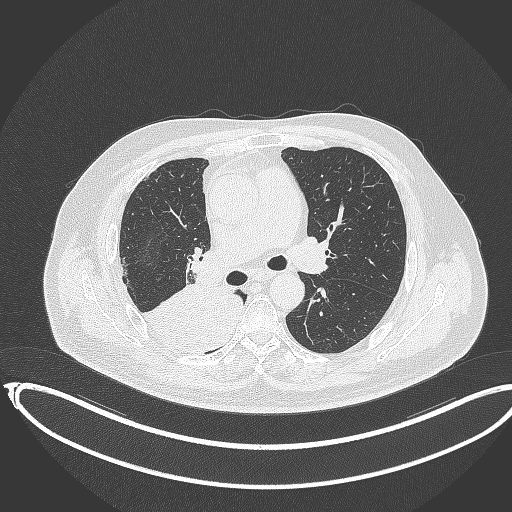
Chest CT, one axial slice. Position 211 of 403 along the scan axis. 120 kVp. Lung window (W 1500 / L -600 HU). 1 mm slice thickness. 512 × 512 image matrix, field of view 436 × 436 mm. Male patient, age 68 years. From the clinical record (not read from this slice): clinical TNM (as recorded): T2a N0 M0.
Structures marked on this image (rectangle marked by the reading radiologist):
- lung tumour (recorded histology: adenocarcinoma): bounding box [x1, y1, x2, y2] px = [142, 283, 243, 351]